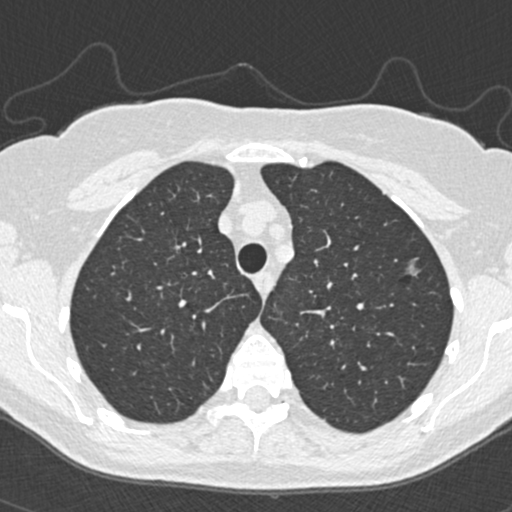
Low-dose screening chest CT, one axial slice. Slice 279 of 350 in the series (ordered by position). Lung window (W 1500 / L -600 HU). 512 × 512 image matrix, field of view 298 × 298 mm.
Outlined on this slice (outlined manually by an expert reader):
- lesion 3 (tumor, upper lobe of left lung): bounding box [x1, y1, x2, y2] px = [407, 263, 419, 277]